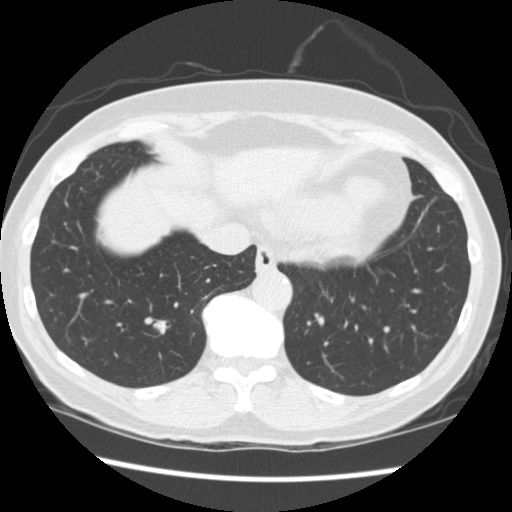
Low-dose screening chest CT, one axial slice; position 70 of 262 along the scan axis; reconstruction kernel STANDARD; 120 kVp; lung window (W 1500 / L -600 HU); 2.5 mm slice thickness; 512 × 512 image matrix.
Structures marked on this image (expert manual segmentation):
- lesion 1 (tumor, lower lobe of right lung): box from (x=154, y=321) to (x=167, y=334) px